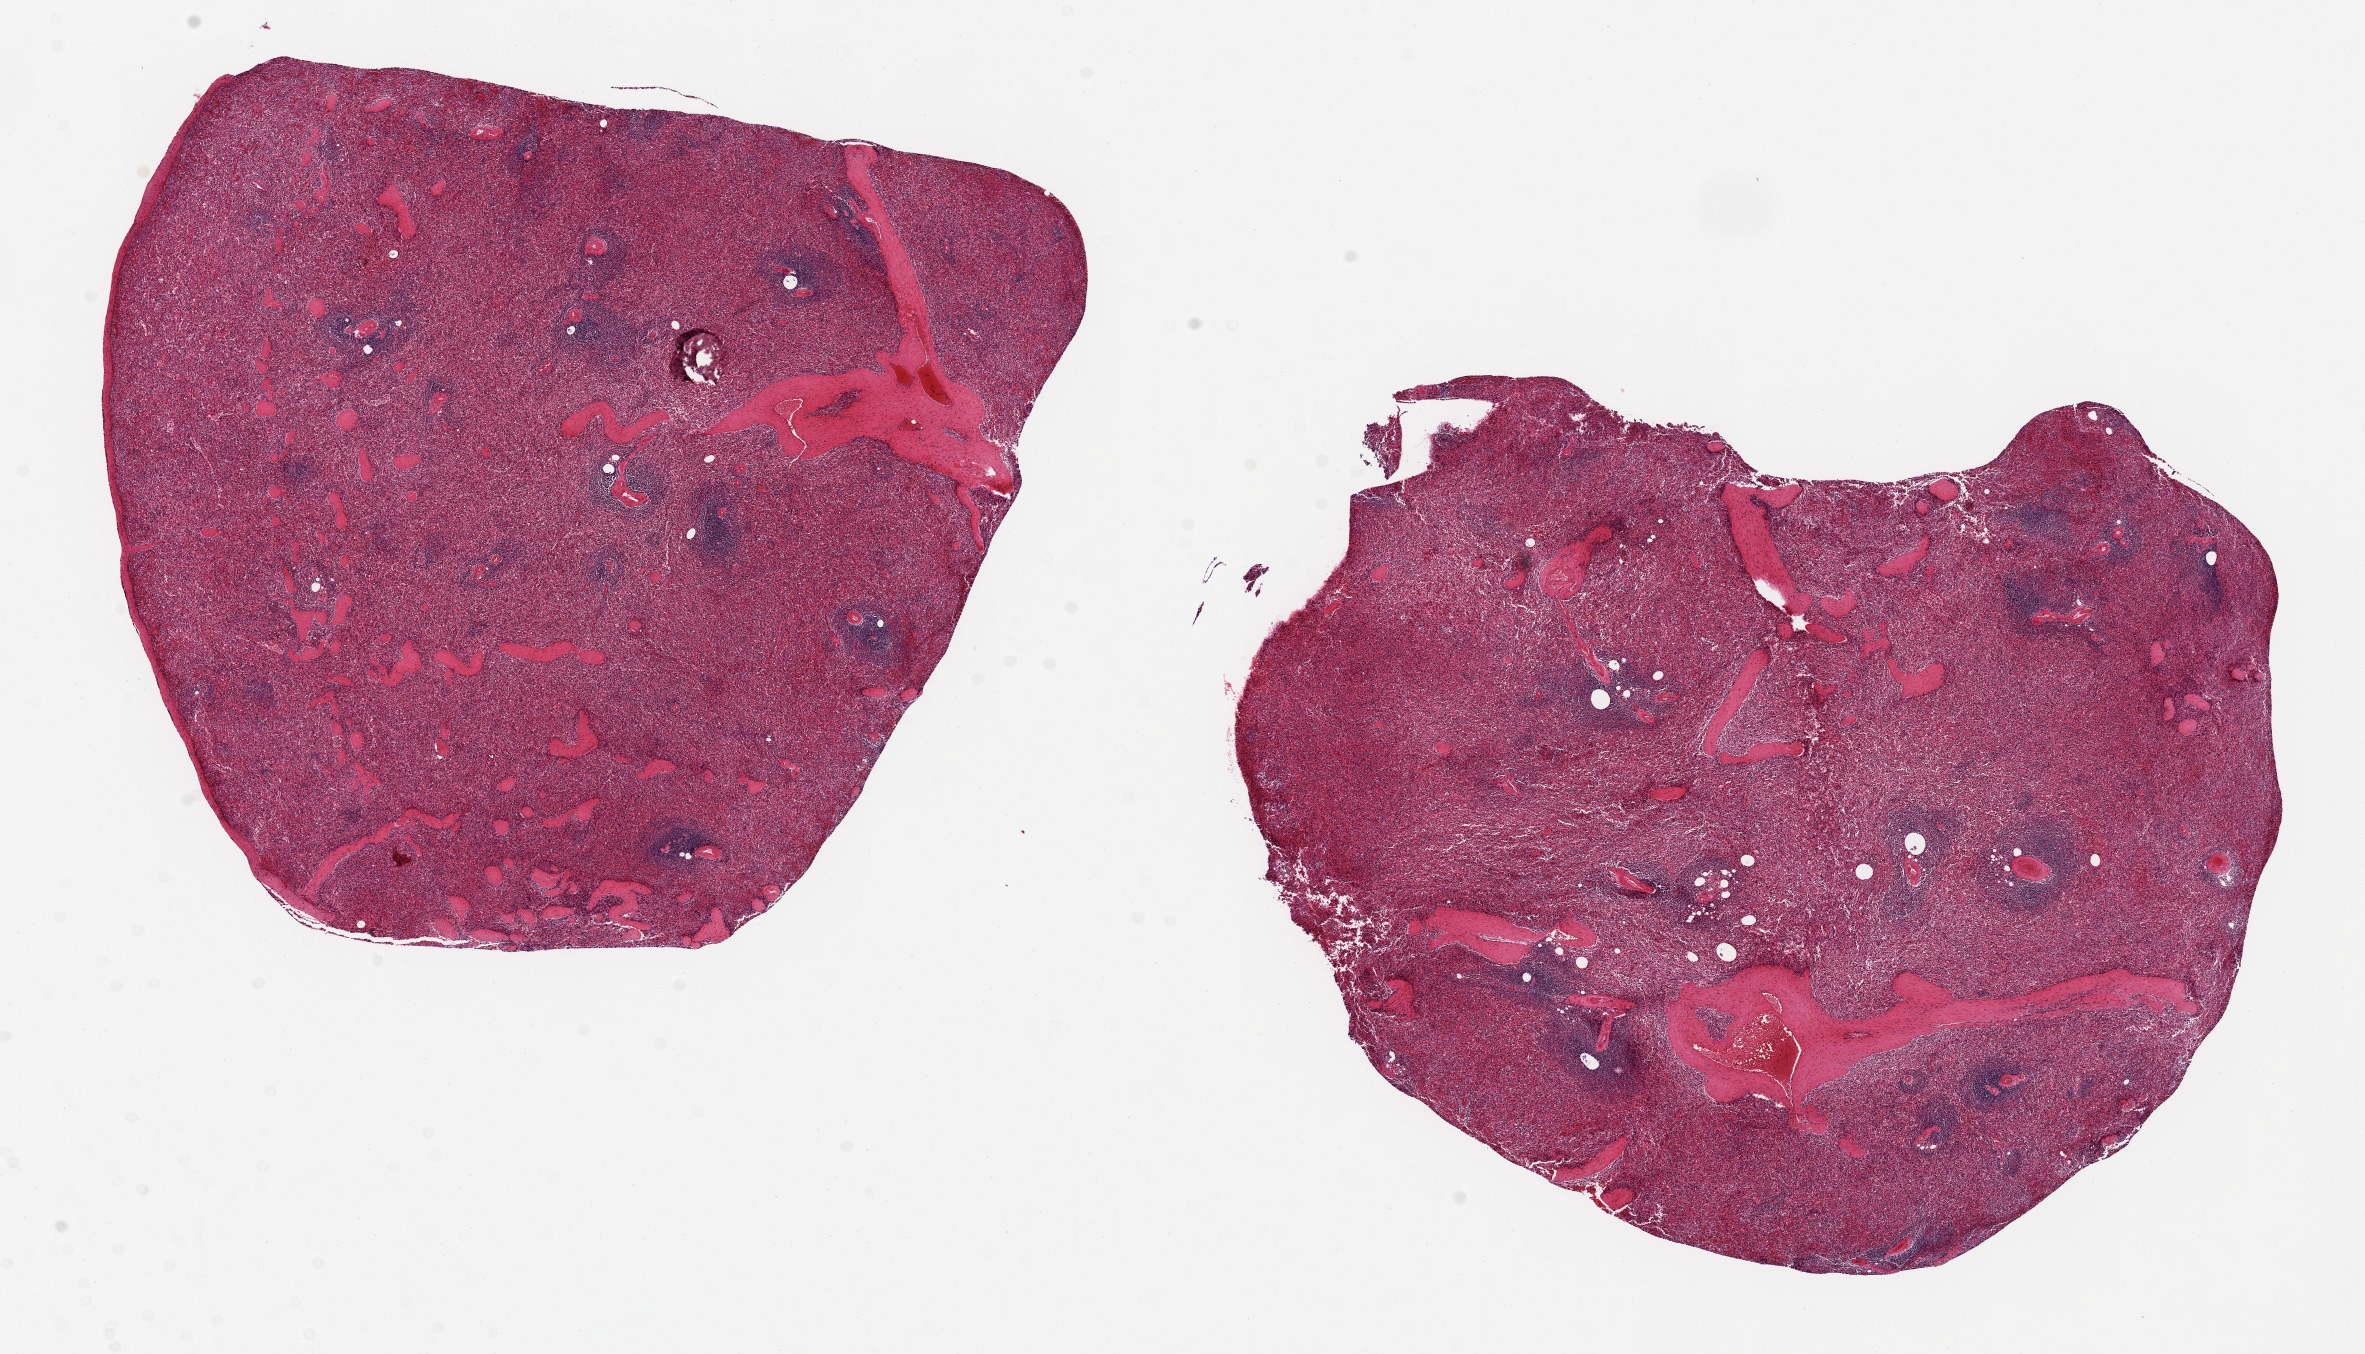
Digitized hematoxylin and eosin (H&E)-stained section — a low-resolution overview of the entire scanned area, about 18.7 x 10.7 mm, PAXgene-fixed, paraffin-embedded tissue, section of spleen (target tissue), donor tissue sample. Donor sex: male.
Review note (as recorded): 2 ~ 7.5x7.0mm aliquots; red pulp especially poorly preserved.